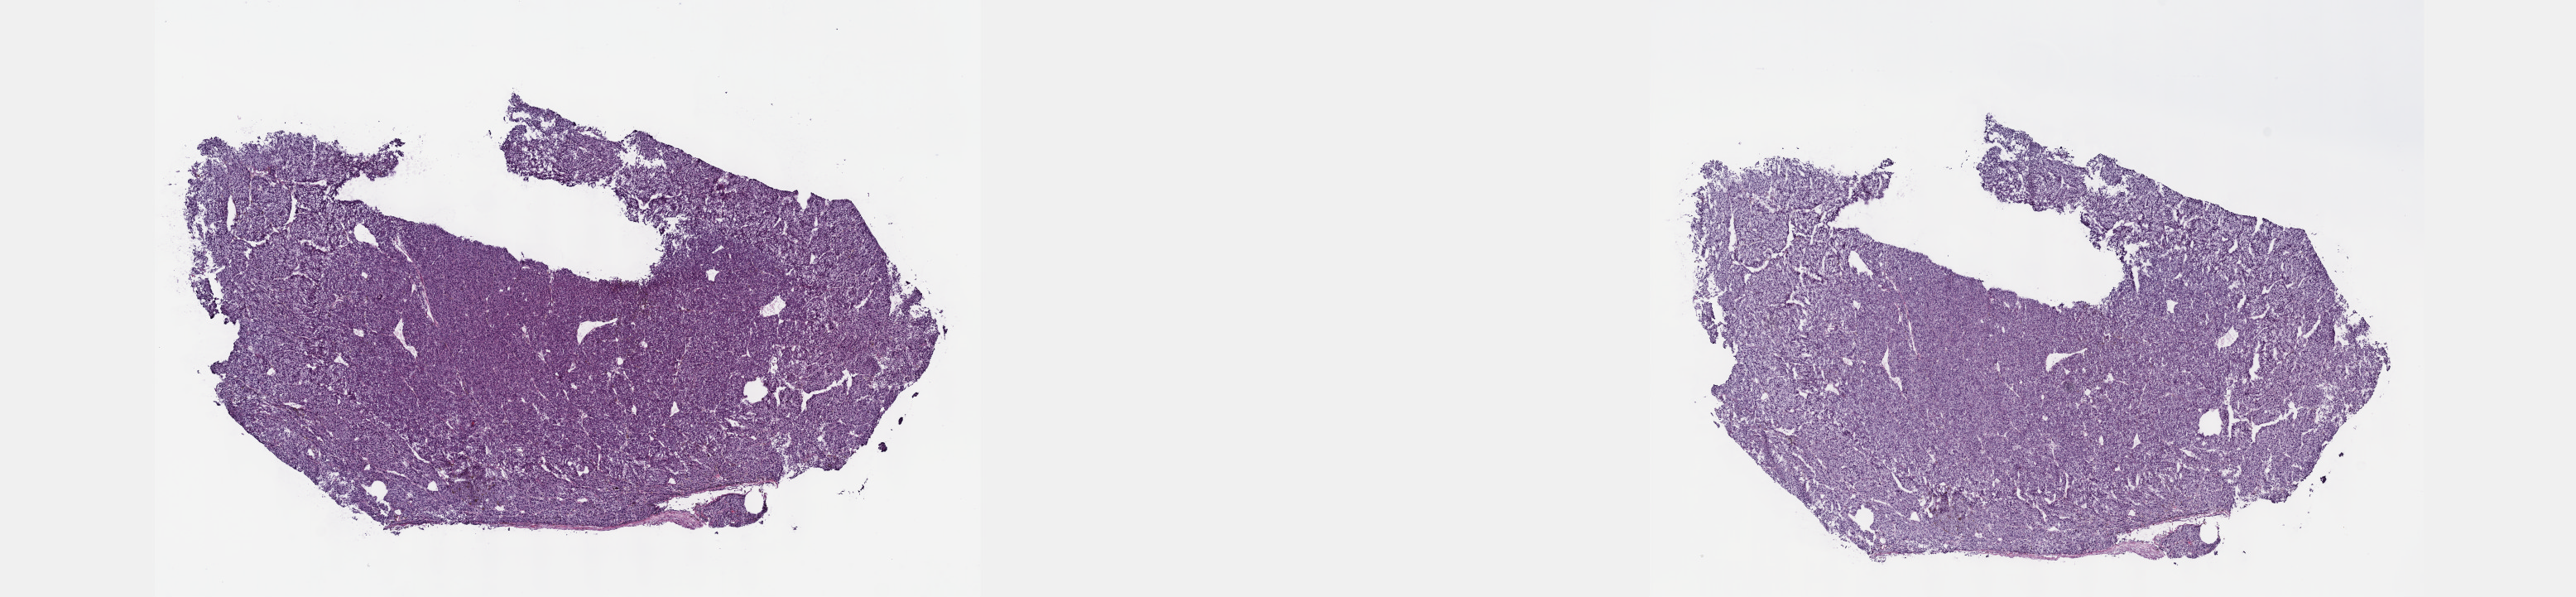
Hematoxylin and eosin (H&E) stained whole-slide image — low-resolution overview of the scanned area, about 25.1 x 5.8 mm. Frozen section from the top of the tissue portion. Primary tumour sample from the uvea. Male patient; age at initial diagnosis 74 years. Composition of this section per pathologist review: tumour cells 100%, tumour nuclei 80%, normal cells 0%, stromal cells 0%, necrosis 0%. Inflammatory infiltration, as recorded: lymphocyte infiltration 2%, monocyte infiltration 0%, neutrophil infiltration 0%.
* TNM: T4a N0 M0
* AJCC pathologic stage: IIIA (7th edition)
* diagnosis: Mixed epithelioid and spindle cell melanoma (ciliary body)